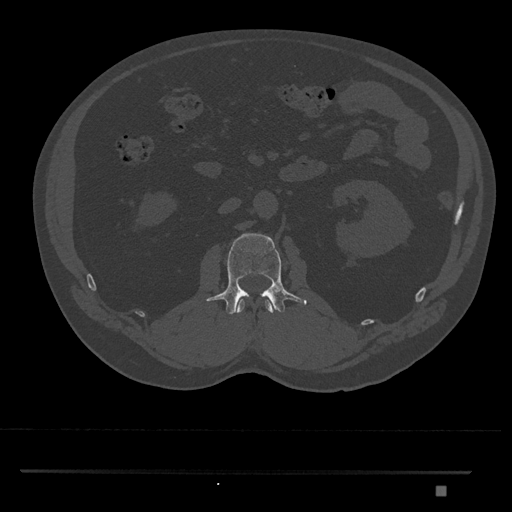
CT including the spine, one axial slice. Position 766 of 1134 along the scan axis. 120 kVp. Bone window (W 1800 / L 400 HU). 512 × 512 image matrix, field of view 429 × 429 mm. Male patient, age 65 years. Case-level facts recorded for this patient, not image findings: primary cancer: prostate.
Annotated regions visible in this slice (semi-automatic segmentation, software-assisted and operator-edited):
- L1 vertebra: bounding box (x1, y1, x2, y2) in pixels: (235, 299, 274, 314)
- L2 vertebra: (206, 233, 307, 315)